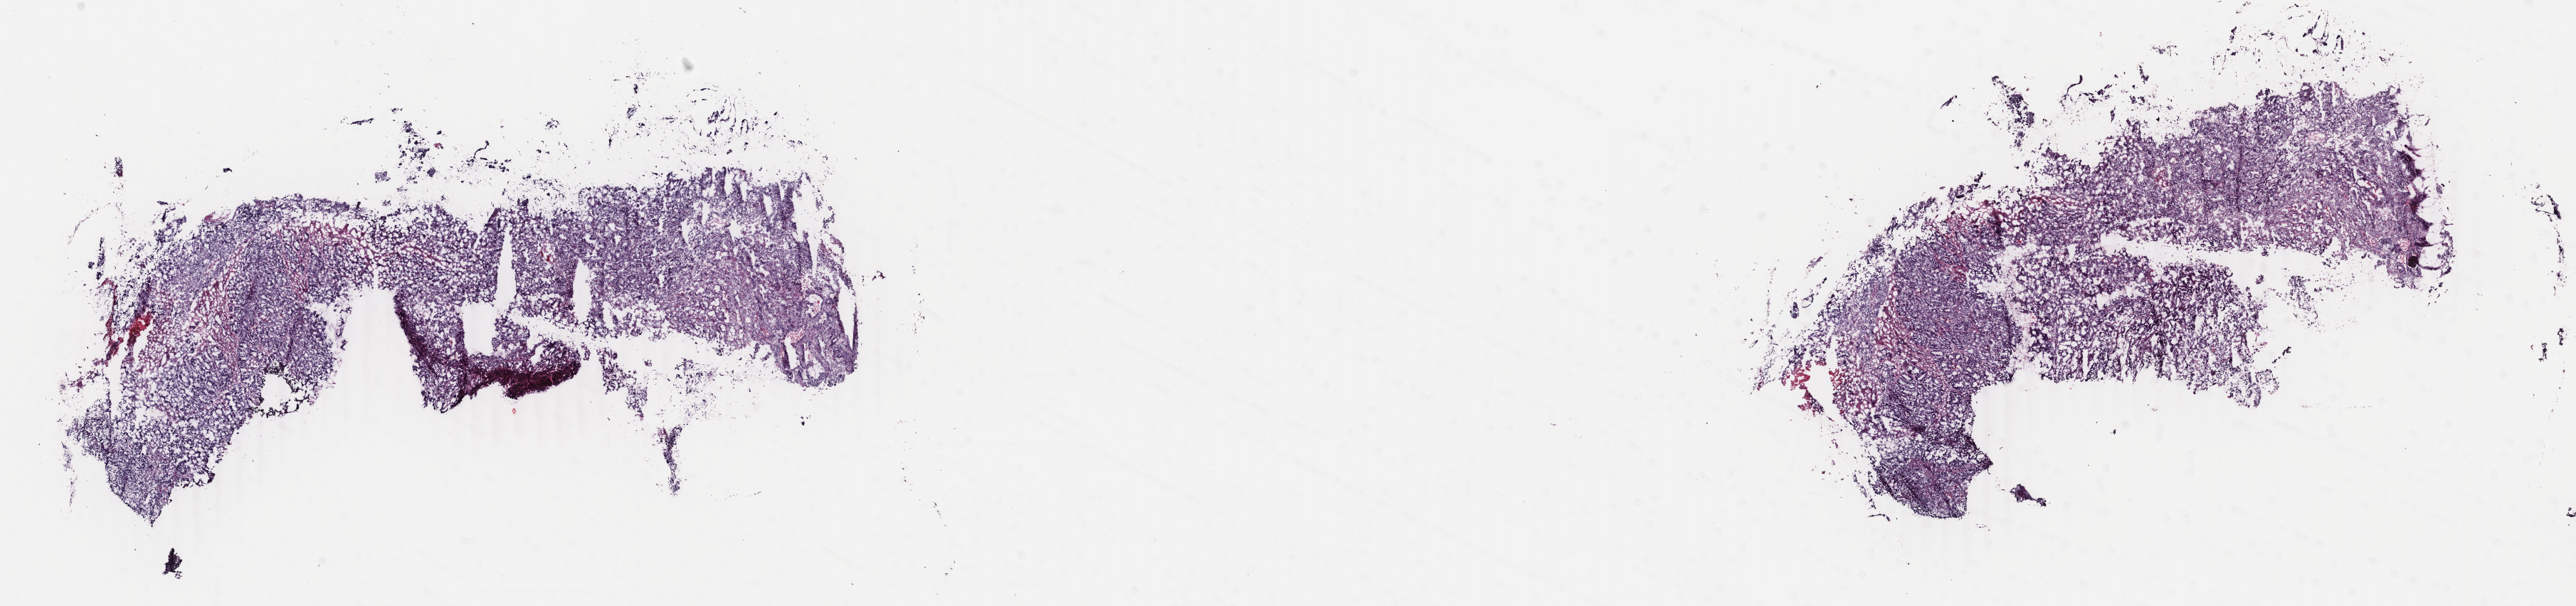
Whole-slide histology image, H&E — whole scanned area (about 28.8 x 6.8 mm) shown as a low-resolution overview. Frozen section. Primary tumour sample from the uterus. Female patient; age at initial diagnosis 68 years. Histologic grade: G2 (moderately differentiated). Pathologist review of this section (percent, as recorded): tumour cells 50%, tumour nuclei 70%, normal cells 30%, stromal cells 0%, necrosis 20%. Infiltration values recorded for this section: lymphocyte infiltration 10%, monocyte infiltration 0%, neutrophil infiltration 20%.
FIGO stage: IIB. Histologic diagnosis: Endometrioid adenocarcinoma, NOS (endometrium).